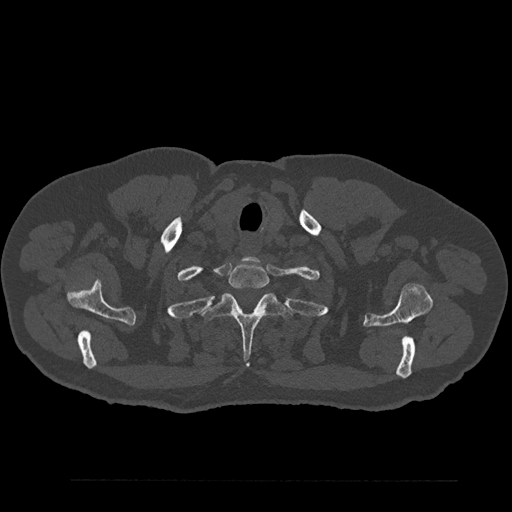
CT including the spine, one axial slice; position 731 of 797 along the scan axis; reconstruction kernel Br40s/3; 120 kVp; bone window (W 1800 / L 400 HU); 512 × 512 image matrix, field of view 430 × 430 mm. Male patient, age 61 years. From the clinical record (not read from this slice): primary cancer: prostate.
Outlined on this slice (semi-automatically segmented with operator editing):
- T1 vertebra: bounding box <228,262,269,290> (left, top, right, bottom; pixels)
- T2 vertebra: <203,293,292,358>